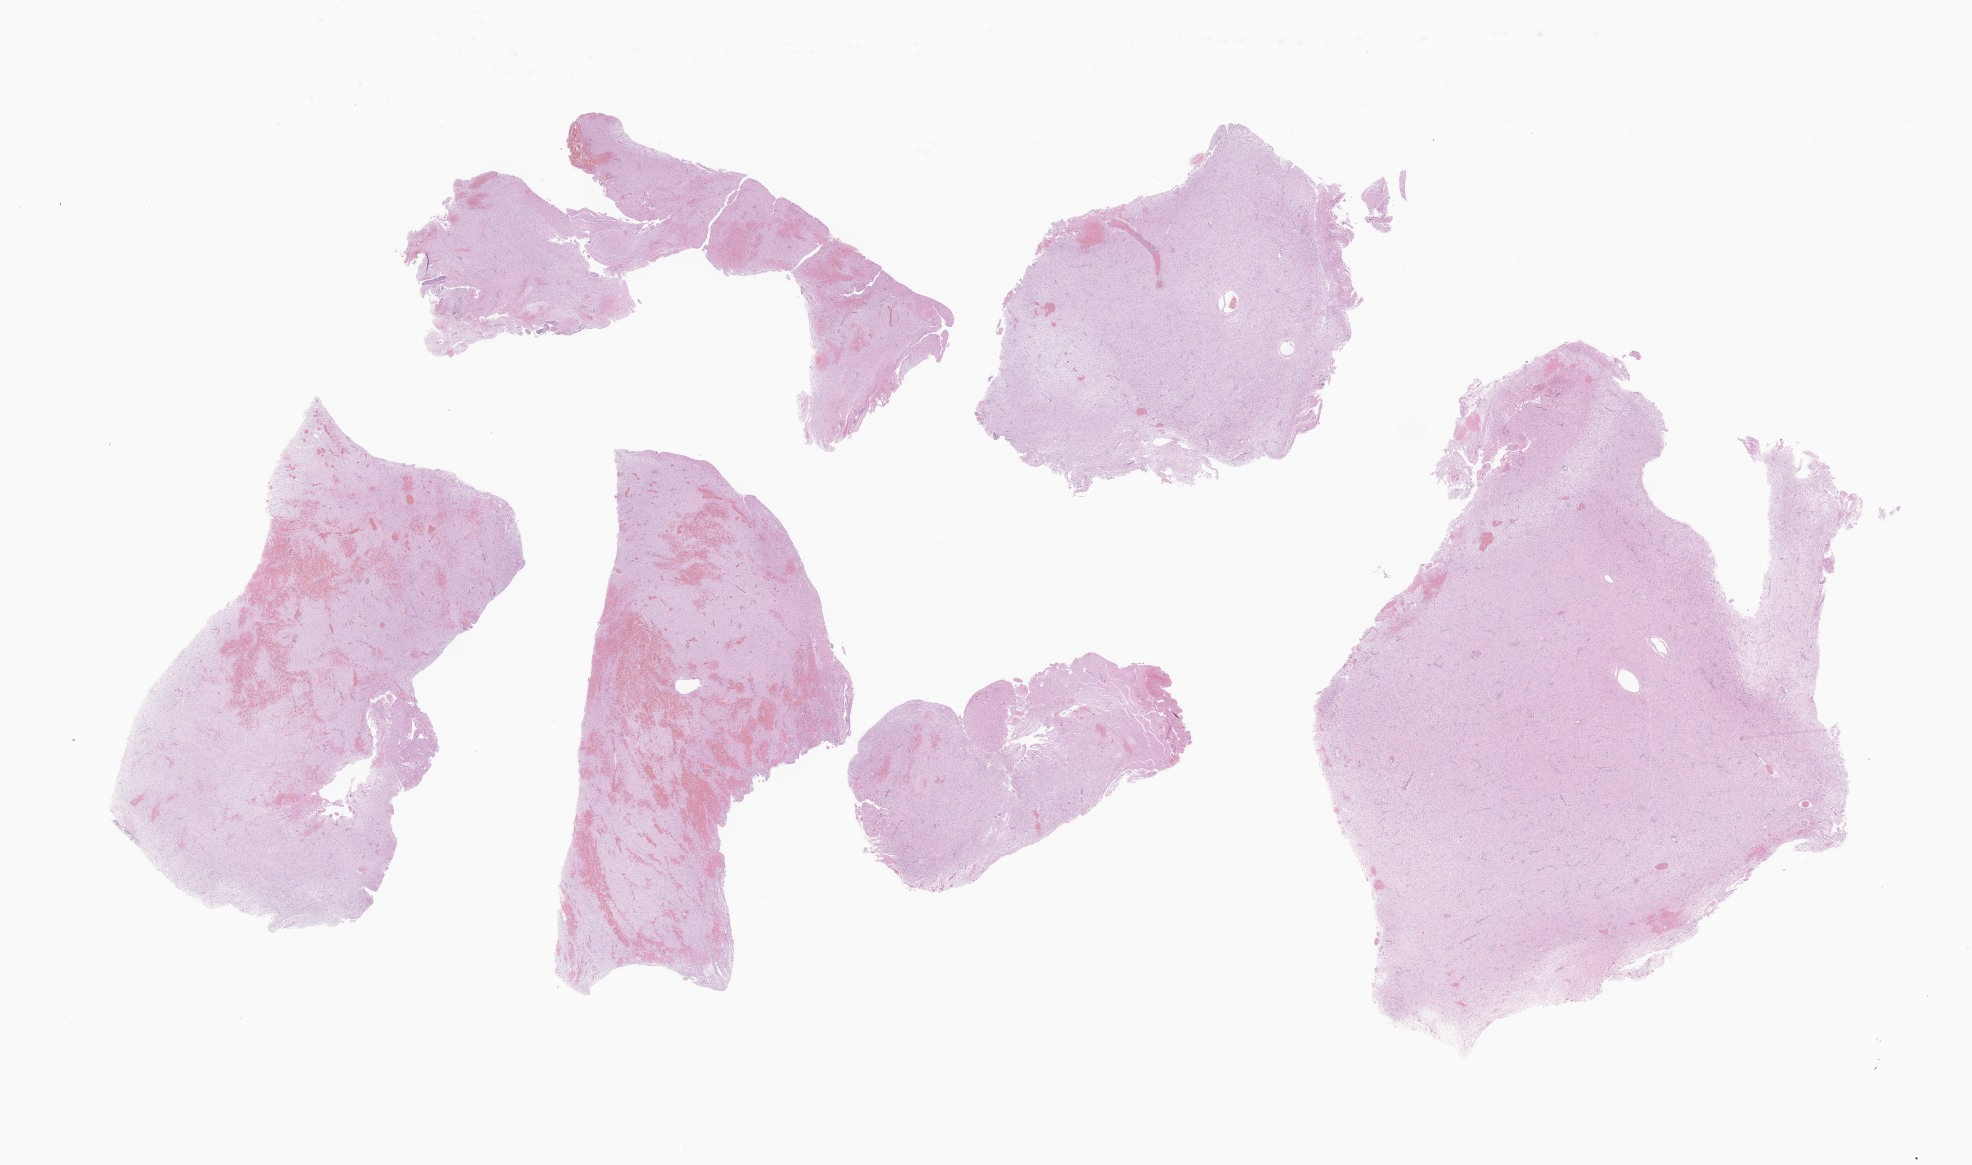
Whole-slide image, H&E stain of tumor tissue from the brain — whole scanned area (about 33.3 x 19.7 mm) shown as a low-resolution overview, formalin-fixed paraffin-embedded section. Patient: female, age 161 months (13 years 5 months).
Recorded diagnosis: Medulloblastoma, NOS.